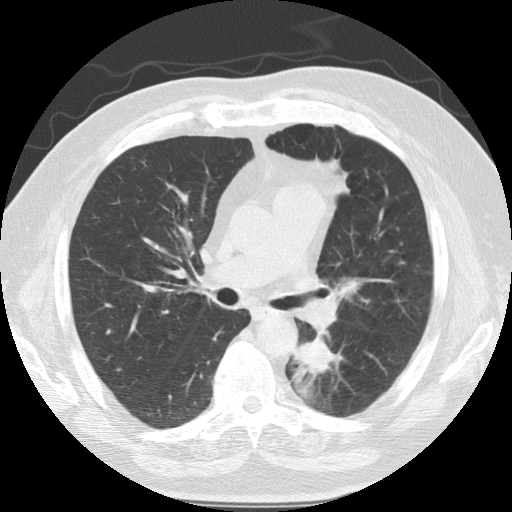
Low-dose screening chest CT, one axial slice; position 71 of 124 along the scan axis; reconstruction kernel STANDARD; 120 kVp; lung window (W 1500 / L -600 HU); 512 × 512 image matrix.
Annotated regions visible in this slice (outlined manually by an expert reader):
- lesion 1 (tumor, lower lobe of left lung): bounding box (x1, y1, x2, y2) in pixels: (292, 339, 335, 401)